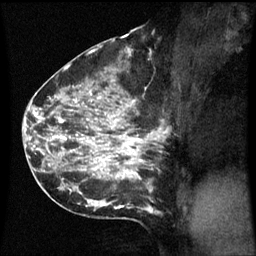
Breast MRI (dynamic contrast-enhanced), one sagittal slice. Slice 33 of 60 in the series (ordered by position). Dynamic contrast-enhanced series, image 2 of 3 at this slice position (ordered by acquisition). 1.5 T. TE 4.2 ms, TR 8.9 ms. 2.1 mm slice thickness. 256 × 256 image matrix, field of view 200 × 200 mm. Female patient, age 42 years. Case-level facts recorded for this patient, not image findings: setting: breast cancer imaged before/during neoadjuvant chemotherapy; receptor status: HER2-positive.
Structures marked on this image (semi-automatic segmentation, software-assisted and operator-edited):
- analysis volume of interest (the breast-tissue region the enhancement analysis was run in; not a lesion): box from (x=66, y=82) to (x=169, y=193) px
- tumour enhancement mask (voxels above the 70 % enhancement threshold inside the analysis volume of interest): (x=80, y=96)–(x=157, y=177)